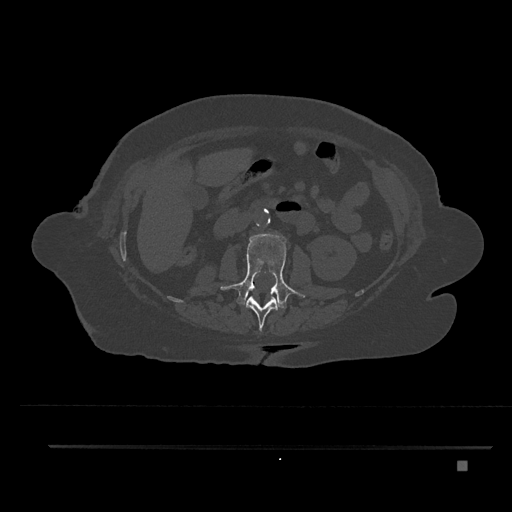
CT including the spine, one axial slice; position 186 of 797 along the scan axis; bone window (W 1800 / L 400 HU); 0.5 mm slice thickness; 512 × 512 image matrix, field of view 437 × 437 mm. Female patient, age 76 years. From the clinical record (not read from this slice): primary cancer: lung.
Structures marked on this image (semi-automatic segmentation, software-assisted and operator-edited):
- L1 vertebra: box from (x=246, y=295) to (x=280, y=331) px
- L2 vertebra: (x=220, y=234)–(x=305, y=309)